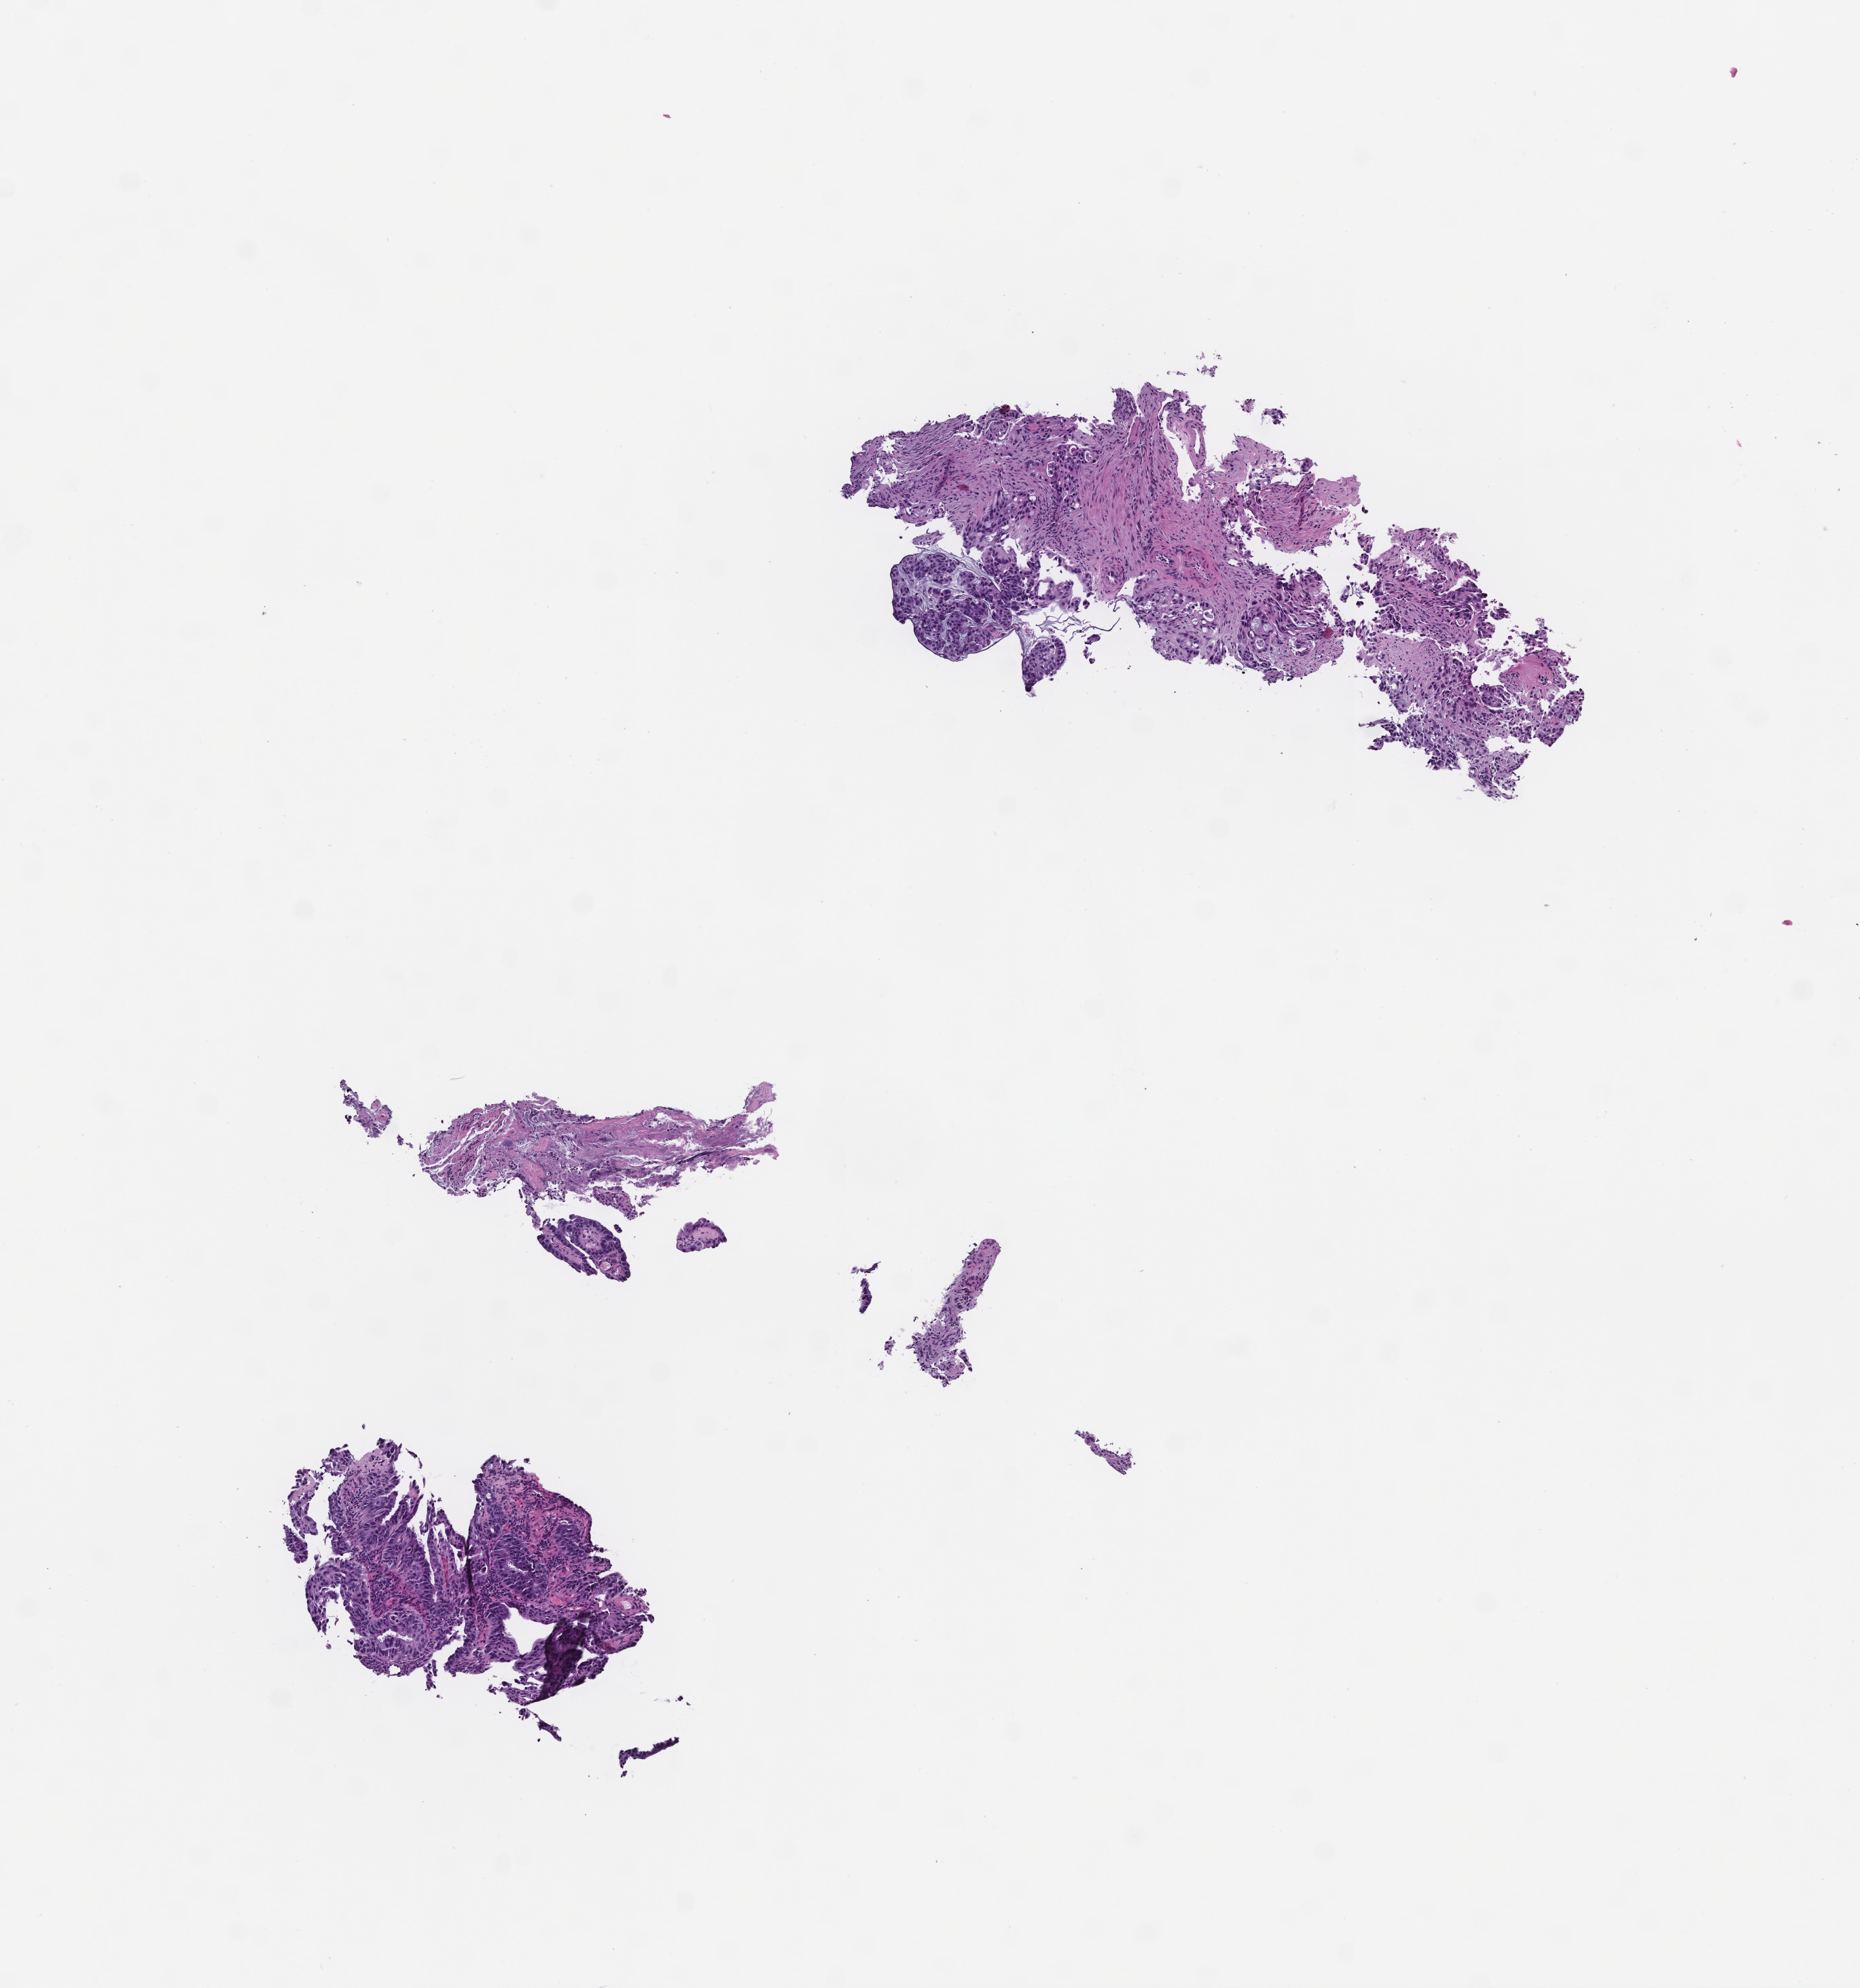
Hematoxylin and eosin (H&E) whole-slide image — shown as a low-resolution overview of the whole scanned area (about 5.5 x 5.9 mm). FFPE section. Tissue site: rectum. Male patient.
• this section: primary tumour tissue
• diagnosis: Colorectal Carcinoma